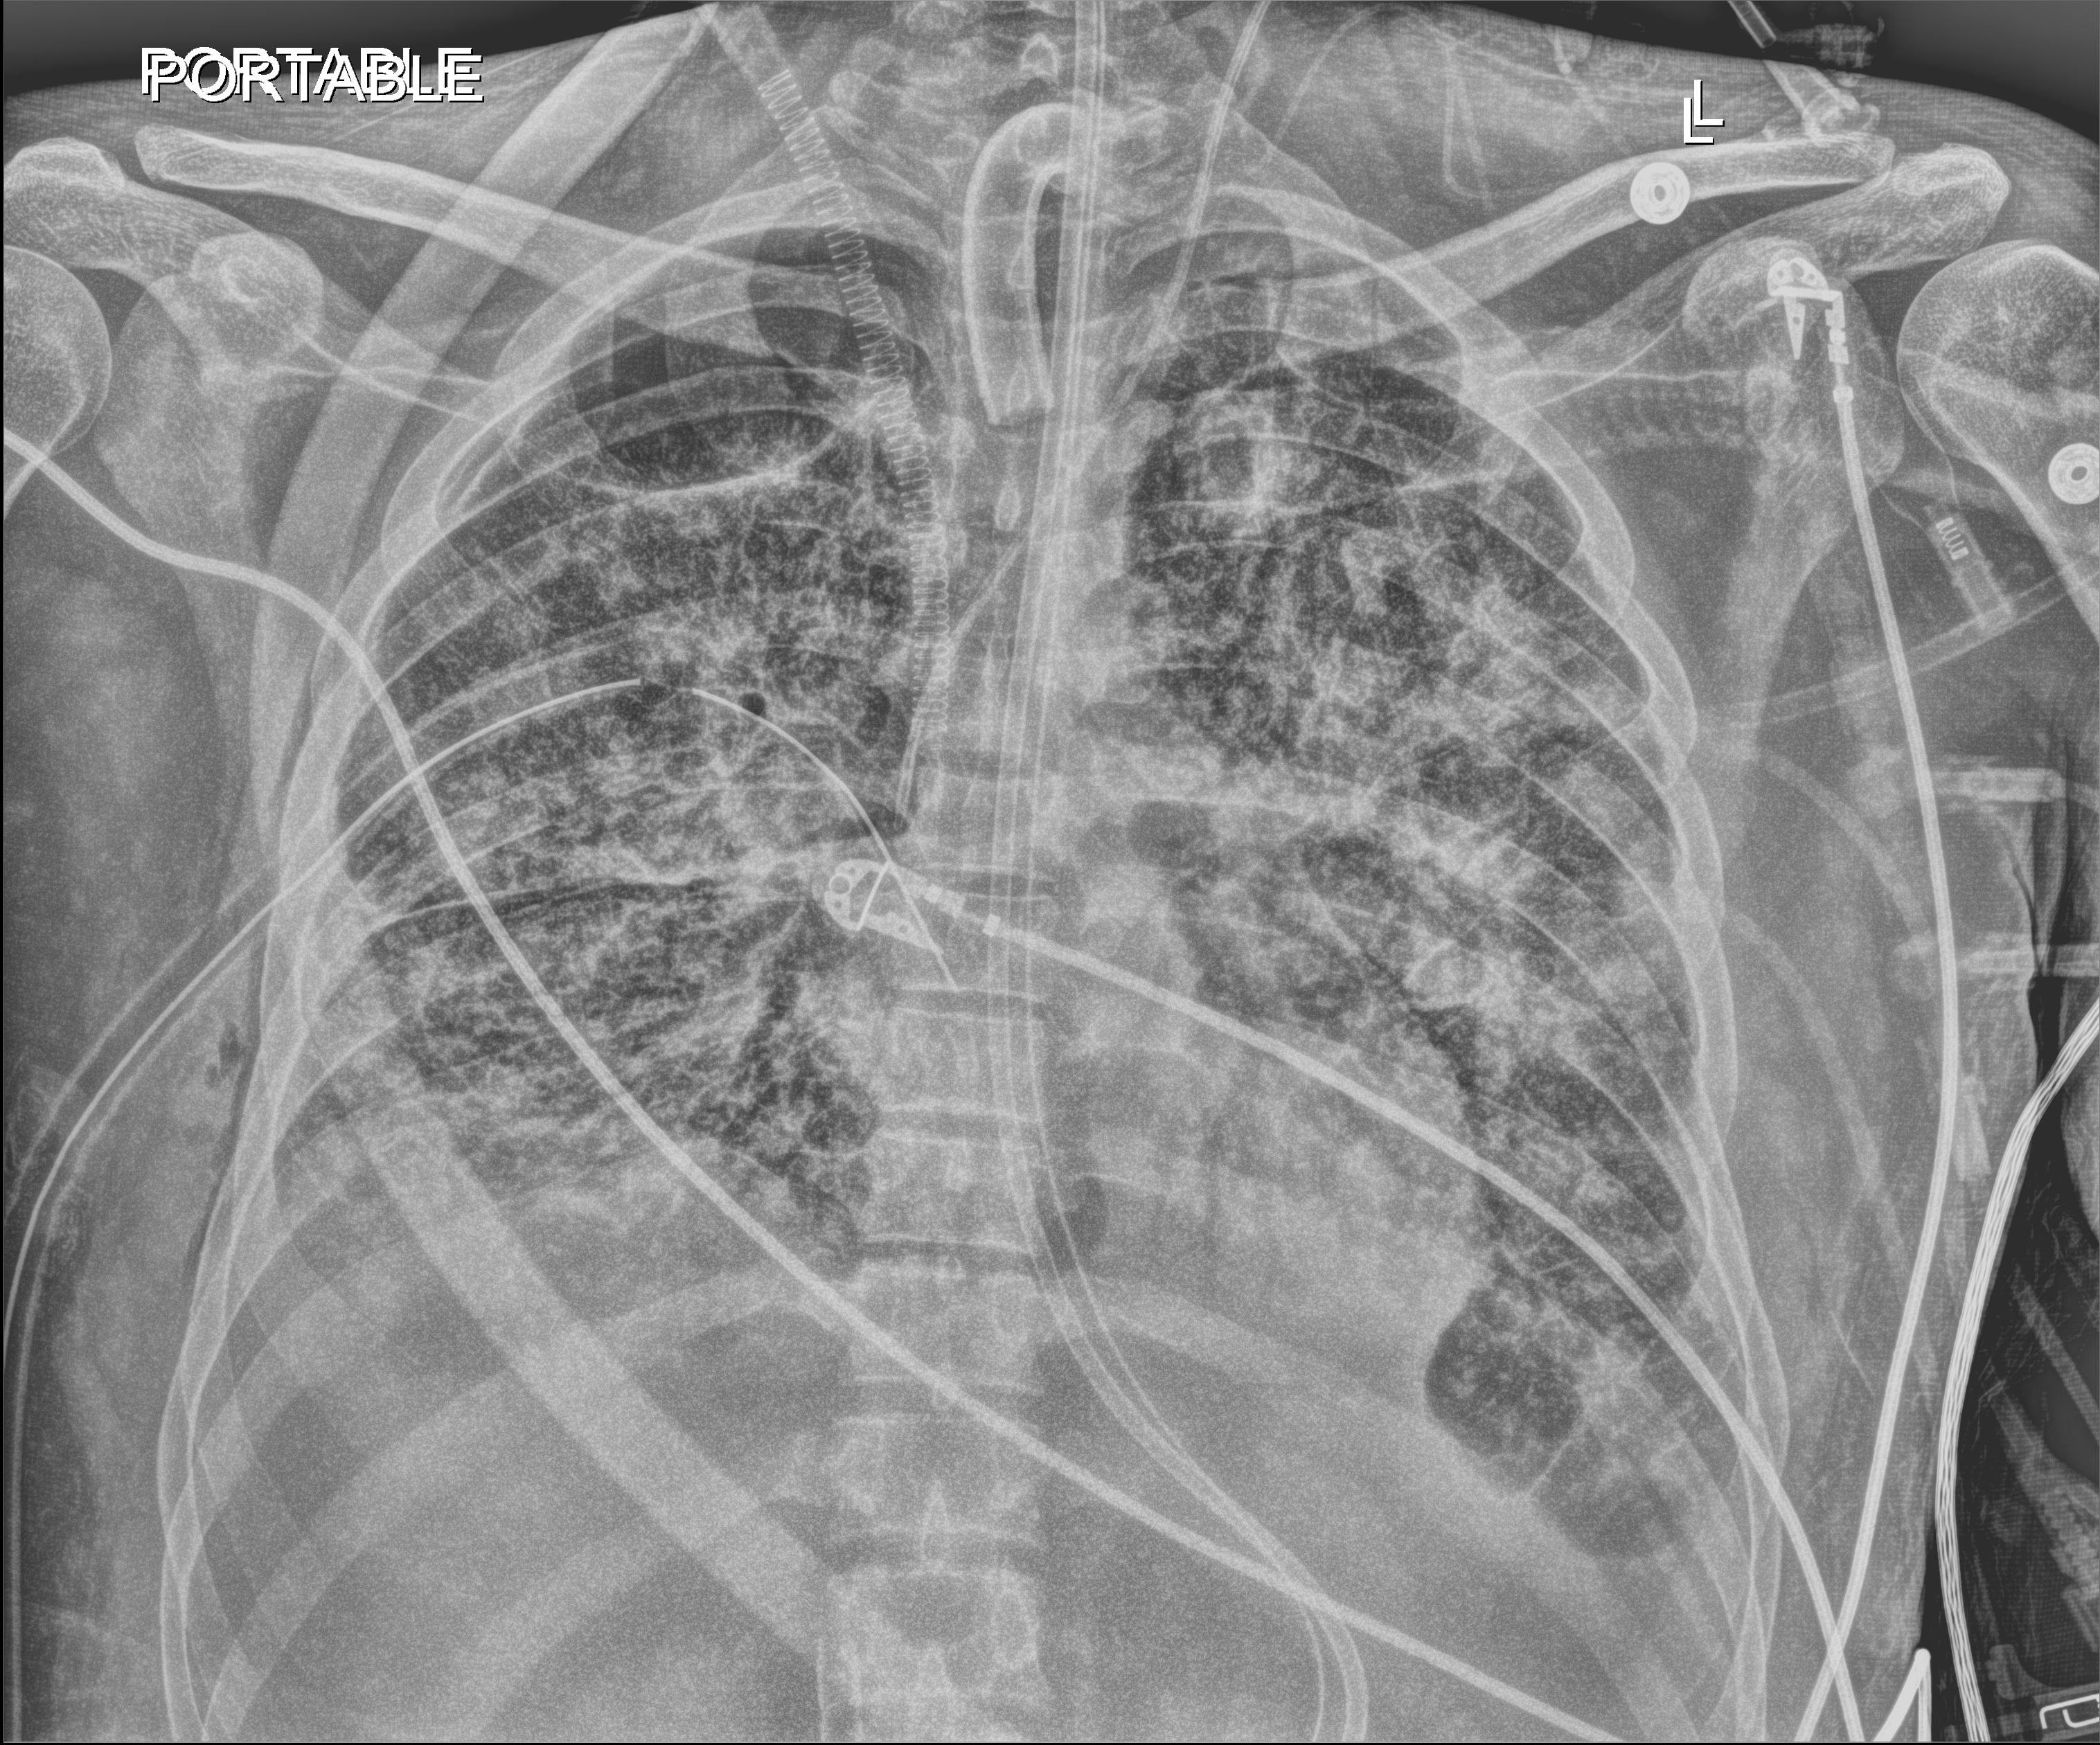
Chest X-ray. Adult patient hospitalised with COVID-19, age 18–59 years.
Hospital-stay facts (about this admission, not read from this image; timing relative to this image not recorded):
- mechanically ventilated during this hospital stay: yes